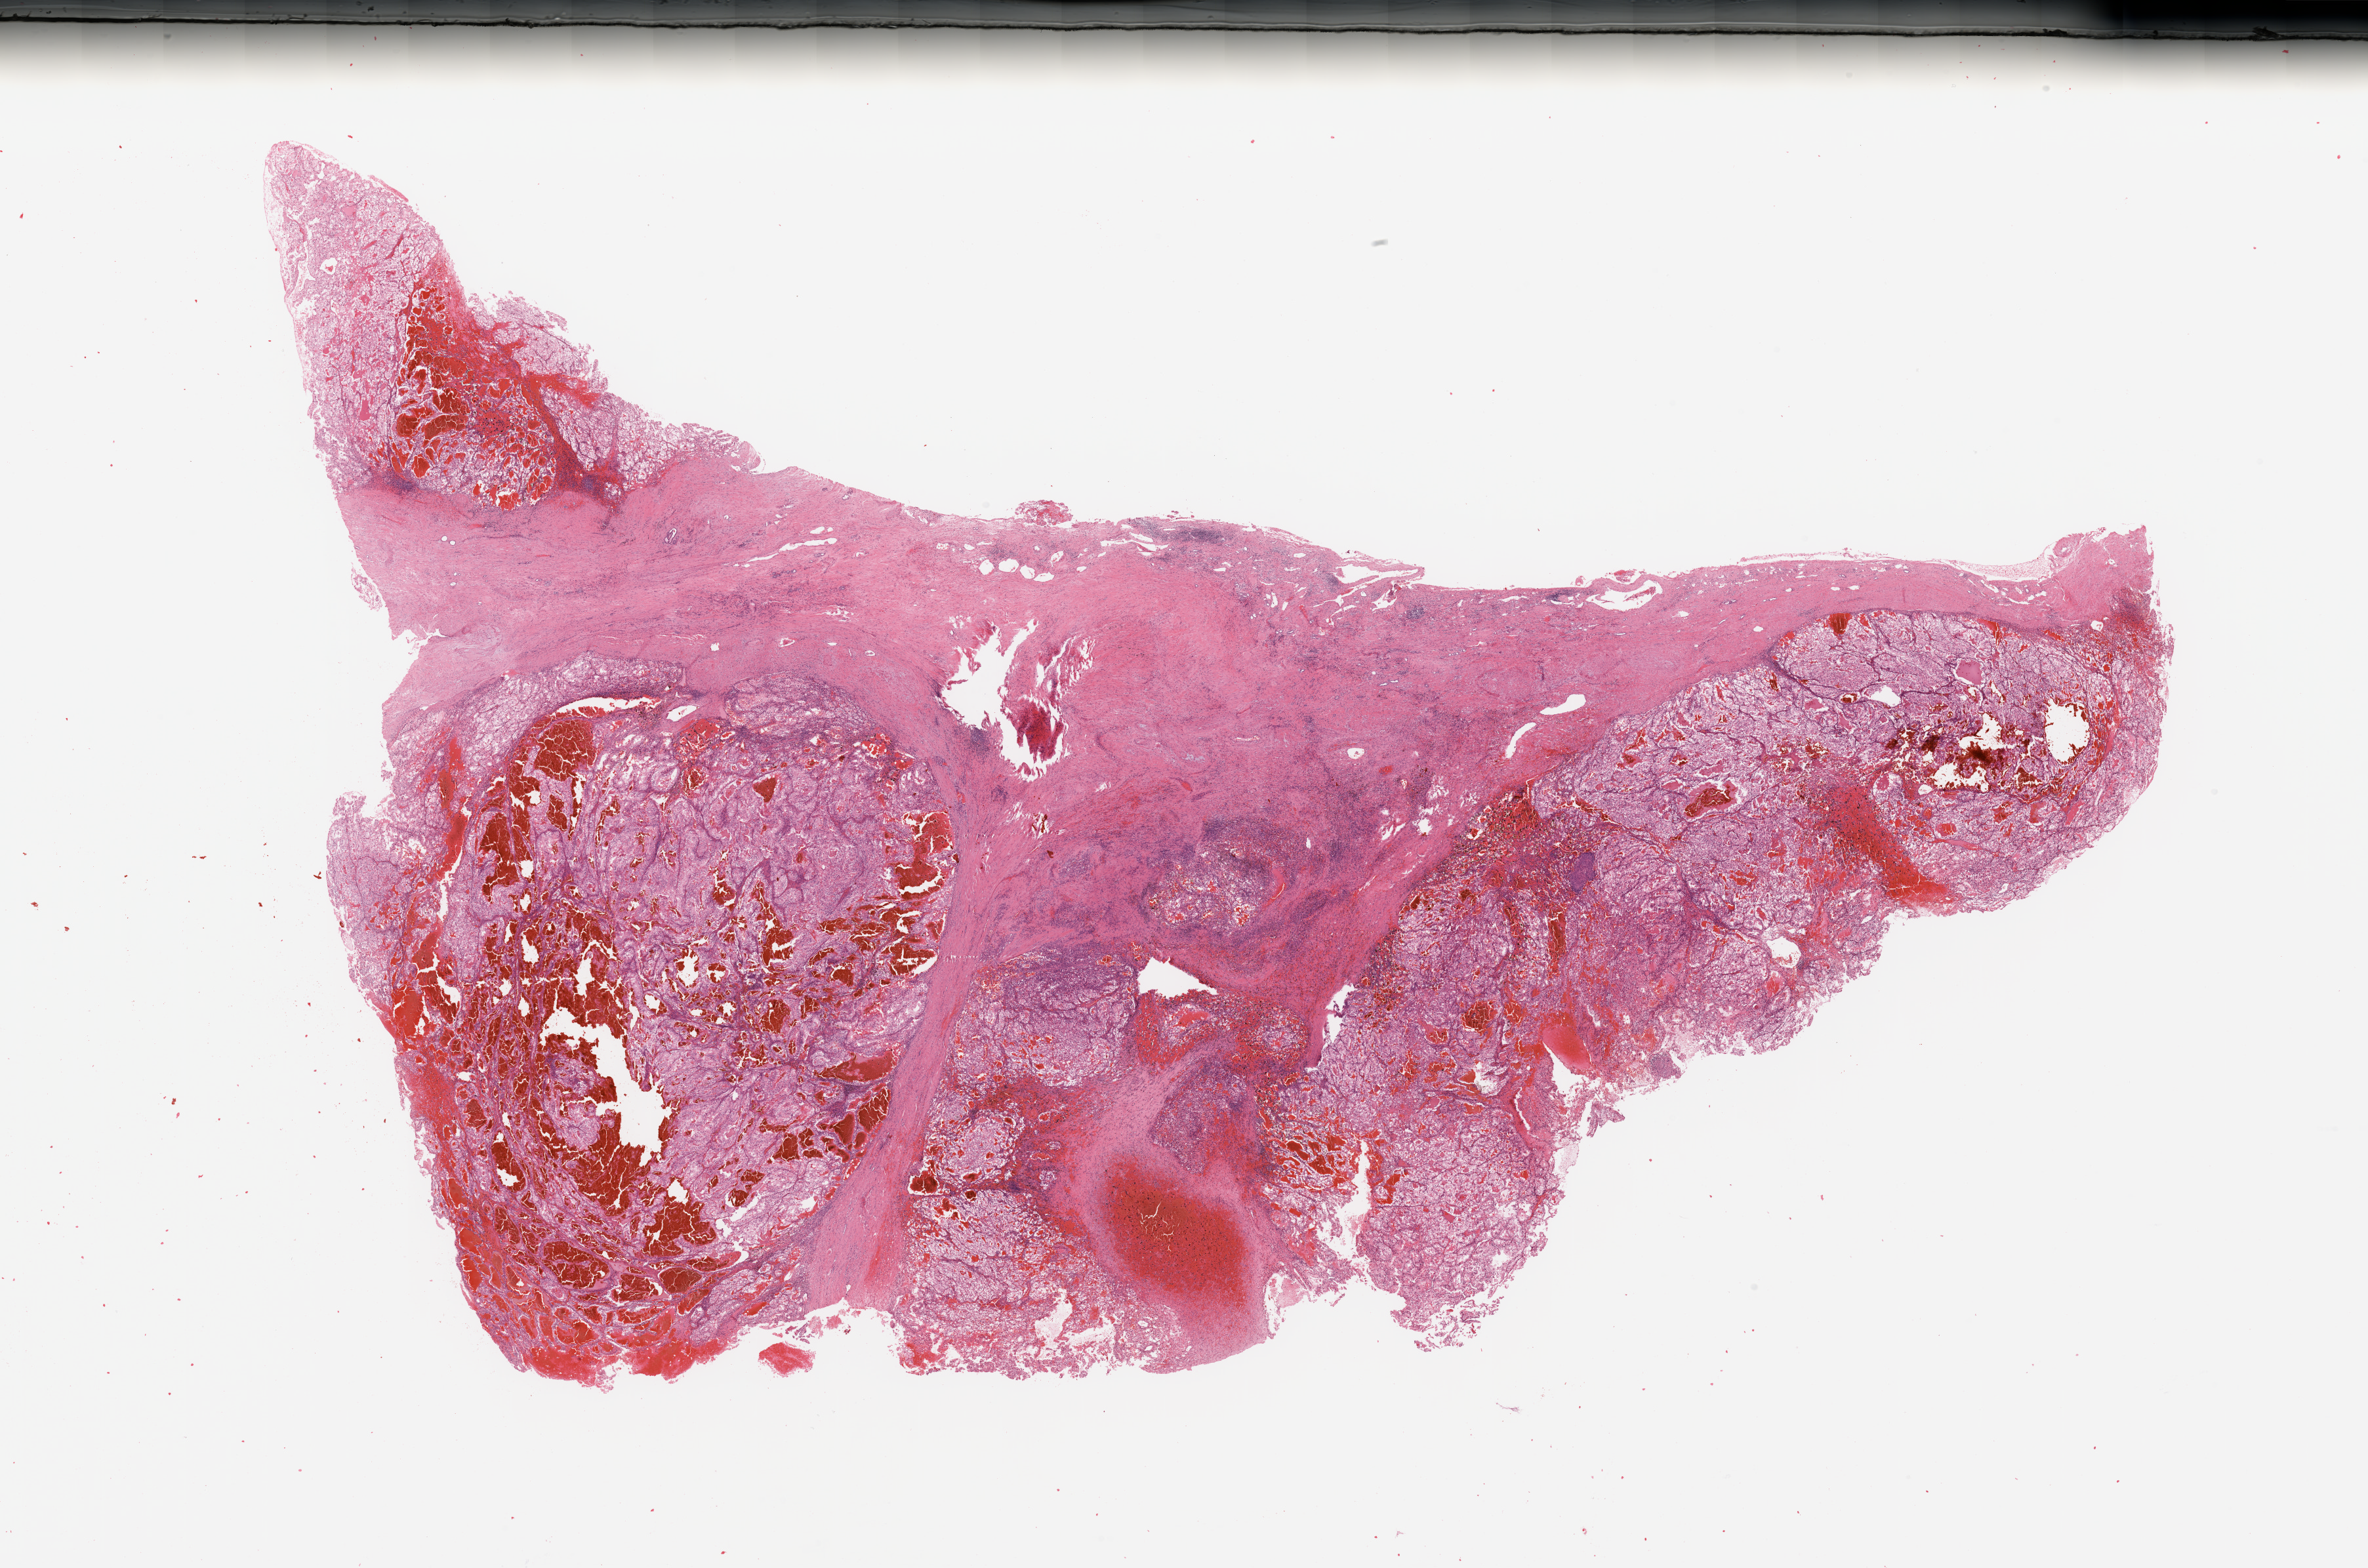
Whole-slide histology image, H&E, a low-resolution overview of the entire scanned area, about 28.5 x 18.9 mm (slide scanned at 20x). Tumour tissue sample, kidney. Female, 54 y/o.
Histologic diagnosis: Renal cell carcinoma, NOS.